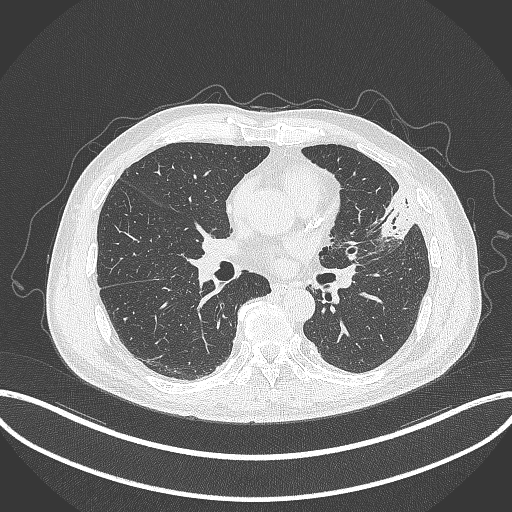
Chest CT, one axial slice; position 165 of 382 along the scan axis; reconstruction kernel B70f; 120 kVp; lung window (W 1500 / L -600 HU); 512 × 512 image matrix, field of view 415 × 415 mm. Male patient, age 64 years. From the clinical record (not read from this slice): clinical TNM (as recorded): T4 N1 M0.
Structures marked on this image (rectangle marked by the reading radiologist):
- lung tumour (recorded histology: adenocarcinoma): bounding box [x1, y1, x2, y2] px = [378, 184, 419, 243]